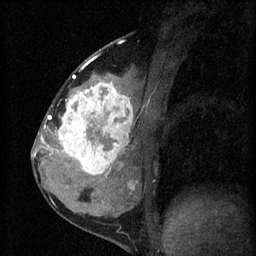
Breast MRI (dynamic contrast-enhanced), one sagittal slice; position 27 of 60 along the scan axis; 3 images stored at this slice position (order not interpretable as contrast timing); 1.5 T; TE 4.2 ms, TR 8.2 ms; 256 × 256 image matrix, field of view 180 × 180 mm. Female patient, age 37 years.
Annotated regions visible in this slice (semi-automatically segmented with operator editing):
- analysis volume of interest (the breast-tissue region the enhancement analysis was run in; not a lesion): bounding box (x1, y1, x2, y2) in pixels: (53, 78, 140, 181)
- tumour enhancement mask (voxels above the 70 % enhancement threshold inside the analysis volume of interest): (55, 78, 133, 177)